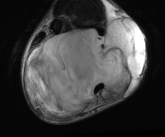
MRI of an extremity soft-tissue mass, one axial slice; slice 24 of 81 in the series (ordered by position); T2-weighted fat-saturated; MR volume resampled by the dataset authors to the PET/CT grid (not the native acquisition matrix); 3.27 mm slice thickness; 165 × 137 image matrix, field of view 161 × 134 mm. Male patient. Case-level facts recorded for this patient, not image findings: histological type: liposarcoma - round cell; grade: high; site of the primary tumour: right calf.
Outlined on this slice (expert contour drawn on MRI and transferred to this co-registered scan by the dataset authors):
- gross tumour volume (mass): bounding box <23,18,145,117> (left, top, right, bottom; pixels)